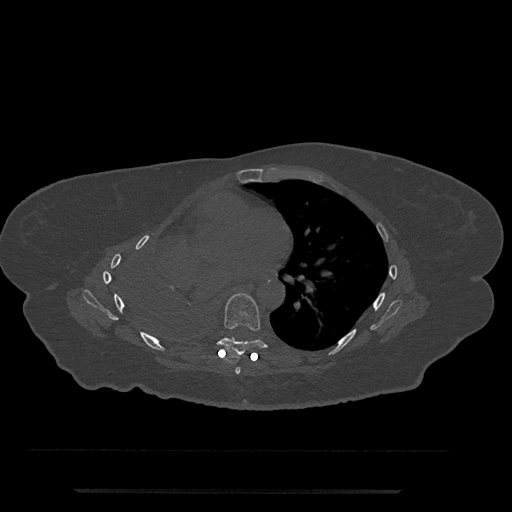
CT including the spine, one axial slice; slice 441 of 797 in the series (ordered by position); reconstruction kernel Br40s/3; bone window (W 1800 / L 400 HU); 0.5 mm slice thickness; 512 × 512 image matrix, field of view 440 × 440 mm. Female patient, age 51 years. From the clinical record (not read from this slice): primary cancer: neuro.
Structures marked on this image (semi-automatic segmentation, software-assisted and operator-edited):
- T6 vertebra: bounding box (x1, y1, x2, y2) in pixels: (235, 367, 241, 374)
- T7 vertebra: (207, 293, 278, 365)